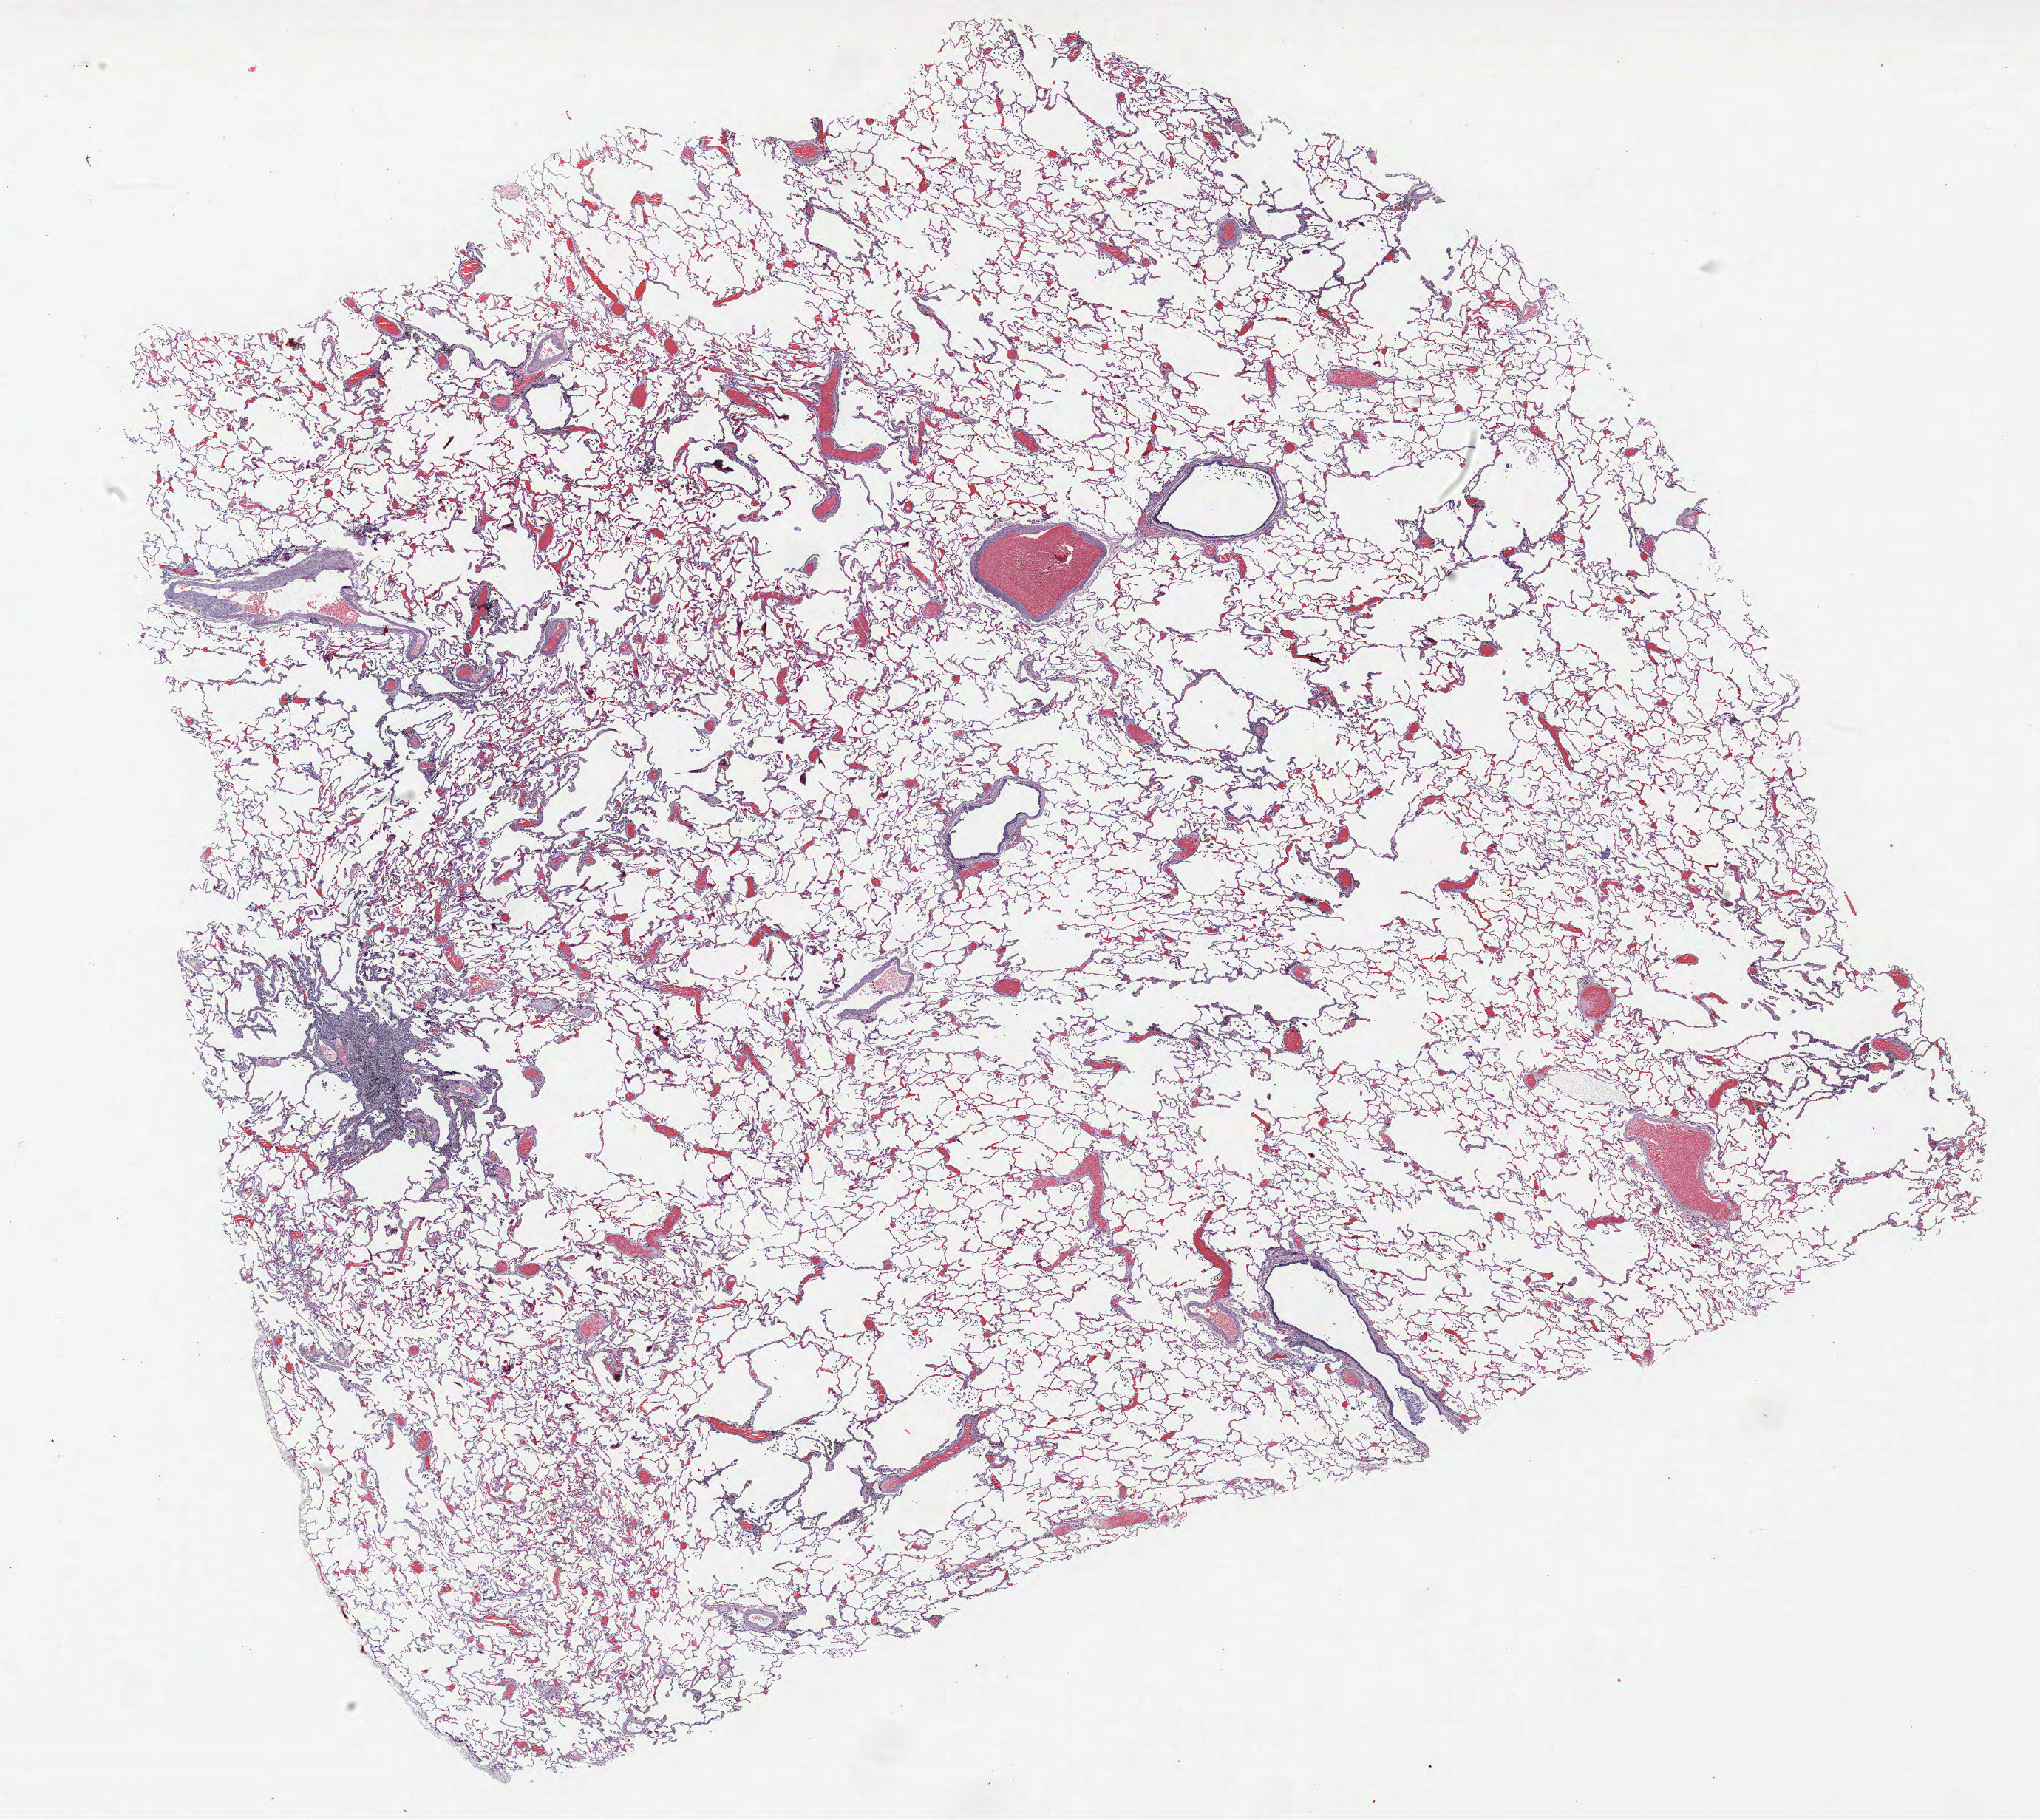
Whole-slide histology image, H&E — whole scanned area (about 22.1 x 19.7 mm, from a 40x scan) shown as a low-resolution overview. Formalin-fixed paraffin-embedded (FFPE) section. Lung tissue. Male, age 62 at enrolment. Grade: poorly differentiated (G3).
Stage (AJCC 6th edition): IB. Participant's lung-cancer diagnosis: Adenocarcinoma, NOS (ICD-O-3 8140/3). Tumour size (pathology): 32 mm. Primary tumour location (clinical record): left upper lobe.